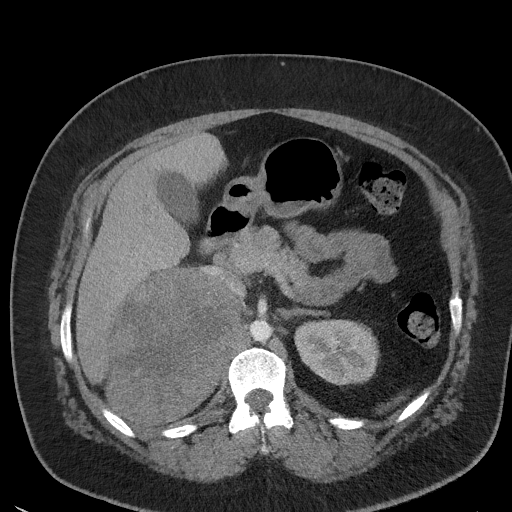
Contrast-enhanced abdominal CT, one axial slice; position 30 of 56 along the scan axis; 120 kVp; intravenous contrast given; soft-tissue window (W 400 / L 40 HU); 5 mm slice thickness; 512 × 512 image matrix, field of view 373 × 373 mm. Patient: female, 35 years. Case-level facts recorded for this patient, not image findings: diagnosis: adrenocortical carcinoma; tumour side: right adrenal; tumour size at pathology: 15 cm; Ki-67 index: 40 %; stage (as recorded): 2.
Annotated regions visible in this slice (semi-automatically segmented with operator editing):
- mass: bounding box (x1, y1, x2, y2) in pixels: (109, 272, 239, 423)